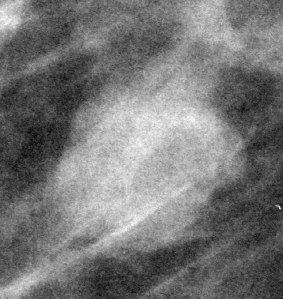
Cropped region of a digitized screen-film mammogram centred on a radiologist-marked abnormality, left breast, CC view, BI-RADS breast density category 2 (scale 1–4).
Mass, shape lobulated, margins circumscribed; BI-RADS assessment category 4; subtlety rating 5 on a 1 (subtle) to 5 (obvious) scale; pathology (as recorded): benign.